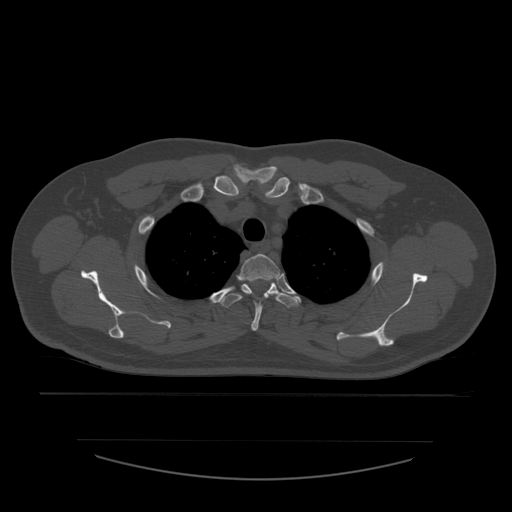
CT including the spine, one axial slice; slice 442 of 532 in the series (ordered by position); reconstruction kernel STANDARD; 120 kVp; bone window (W 1800 / L 400 HU); 512 × 512 image matrix, field of view 441 × 441 mm. Patient age 44 years. From the clinical record (not read from this slice): primary cancer: soft tissue sarcoma.
Outlined on this slice (semi-automatically segmented with operator editing):
- T2 vertebra: bounding box [x1, y1, x2, y2] px = [240, 254, 281, 331]
- T3 vertebra: [217, 277, 299, 308]